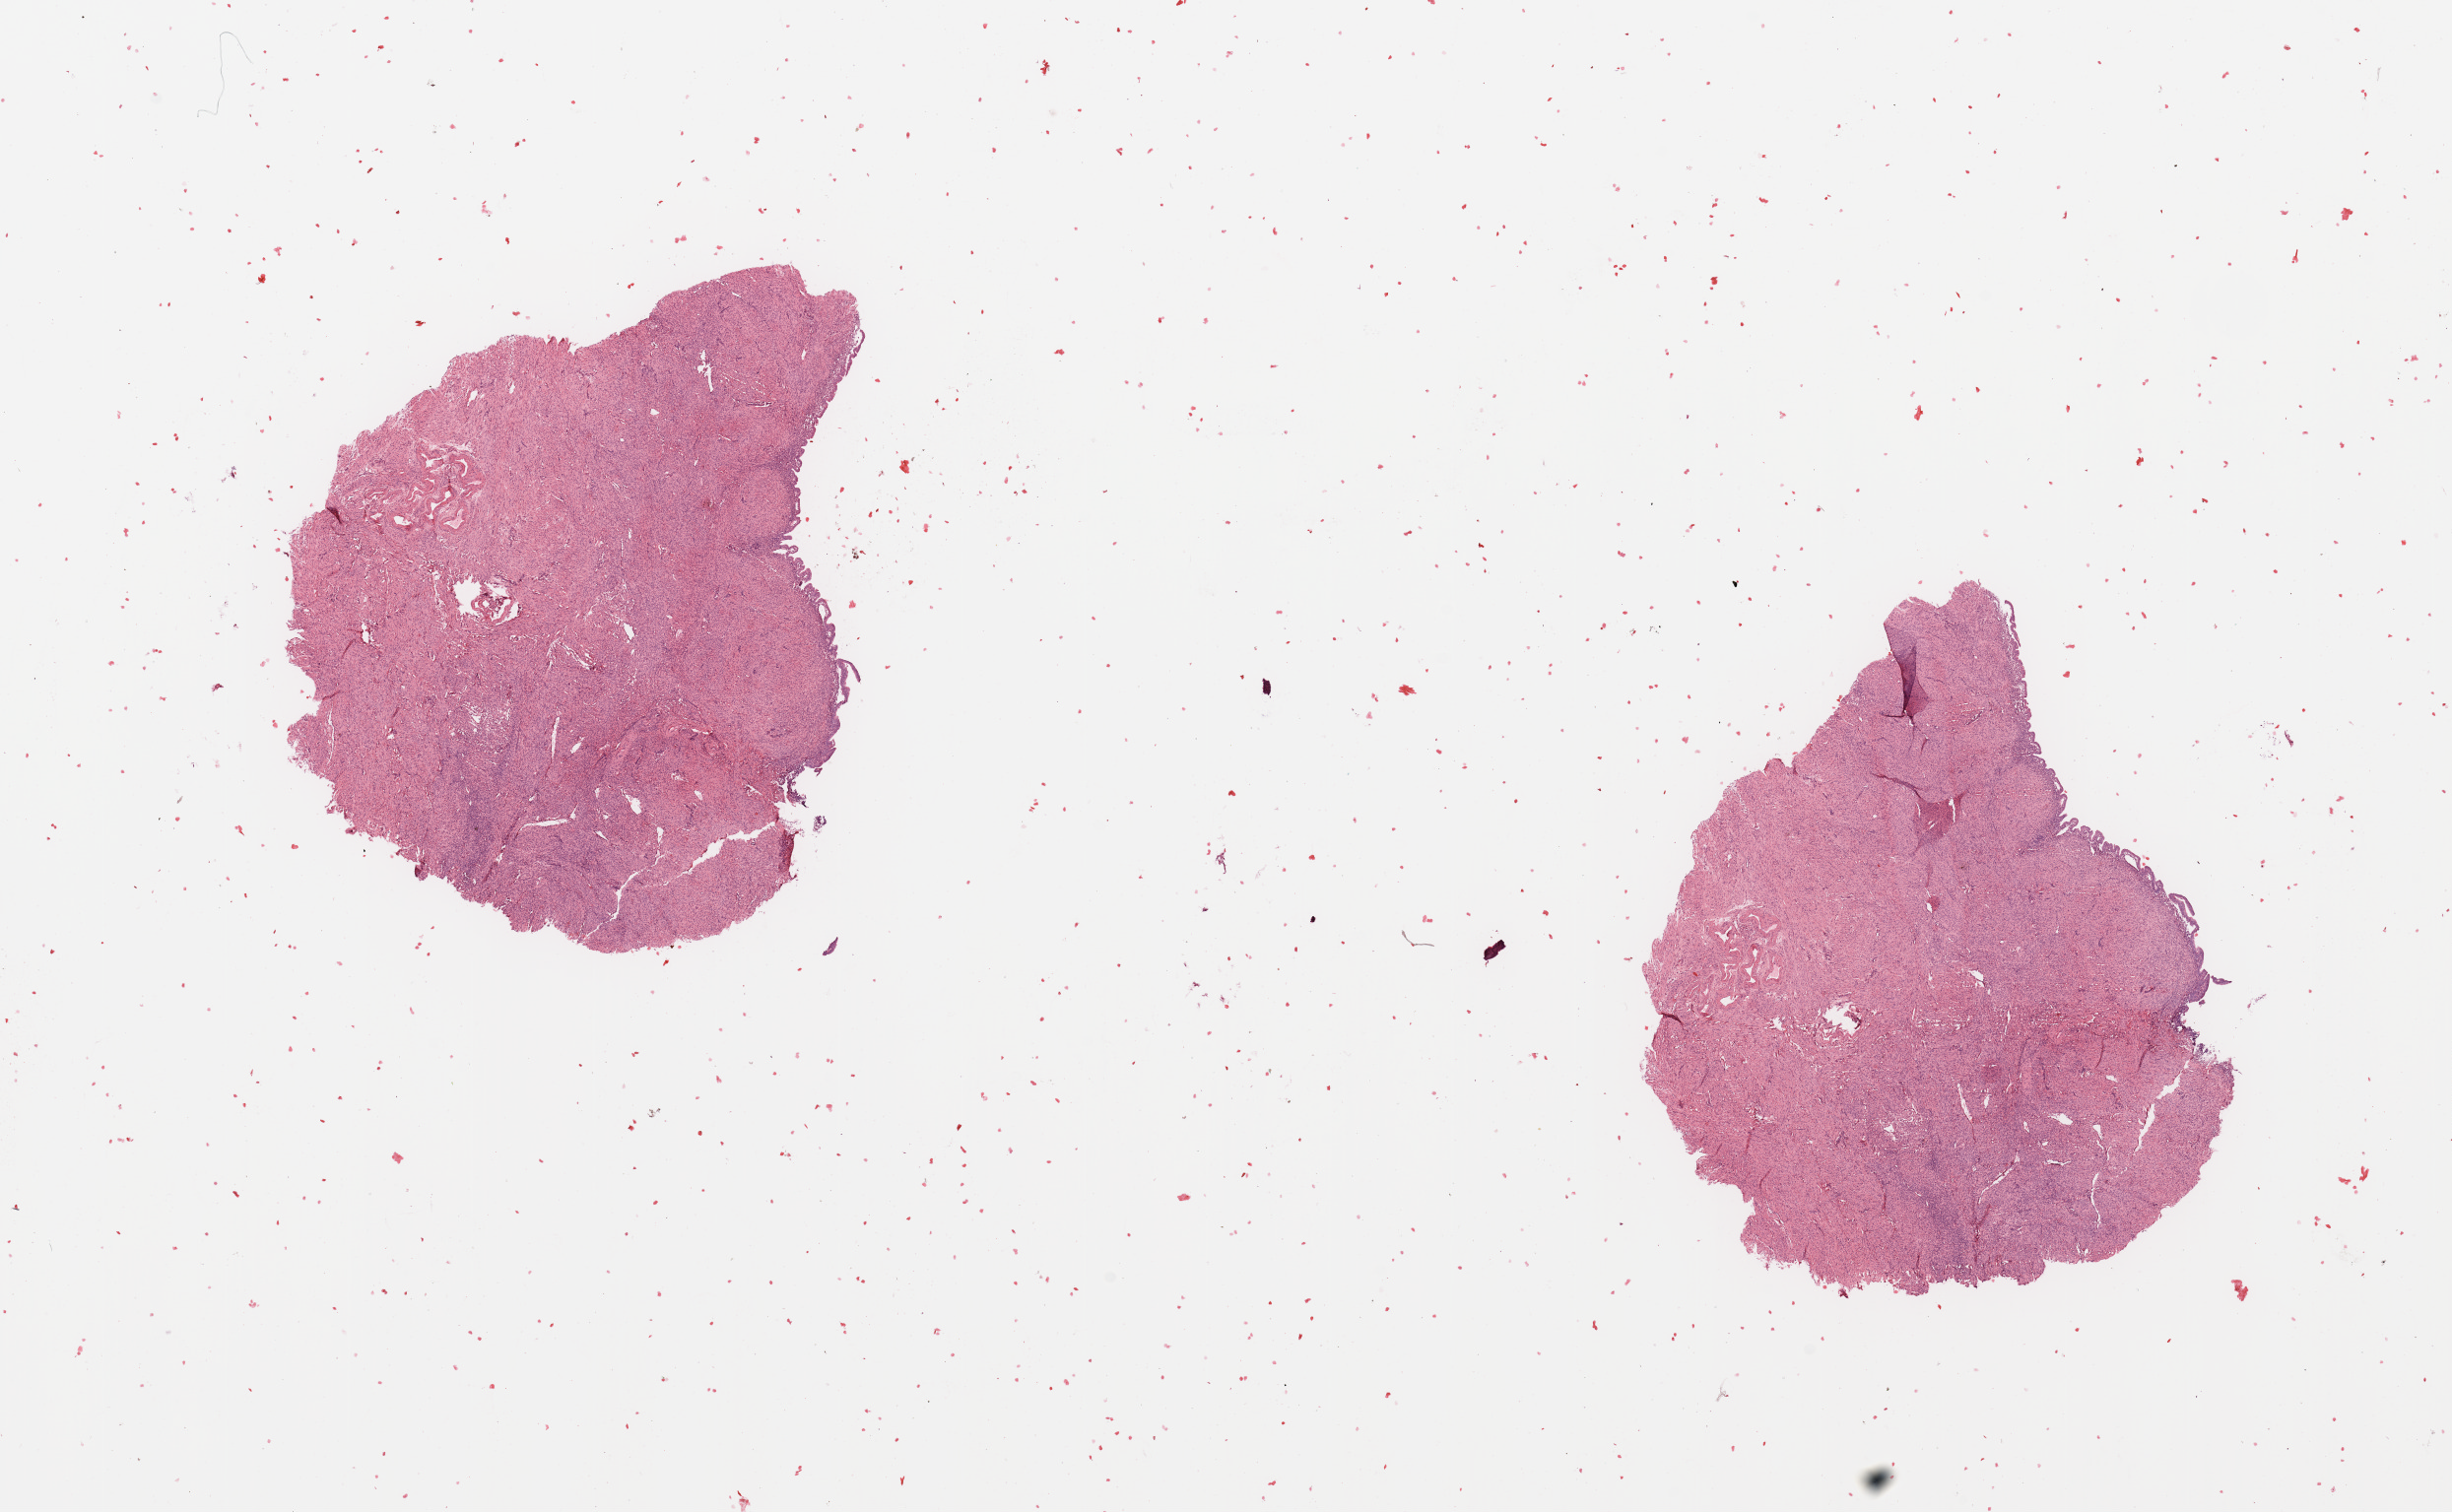
H&E-stained whole-slide image, low-resolution overview of the scanned area, about 19.7 x 12.1 mm (slide scanned at 20x), normal (non-tumour) tissue sample, sampled site: uterus. Female, 65 y/o.
This section: normal (non-tumour) tissue from the same patient. Patient diagnosis: Endometrioid adenocarcinoma, NOS.